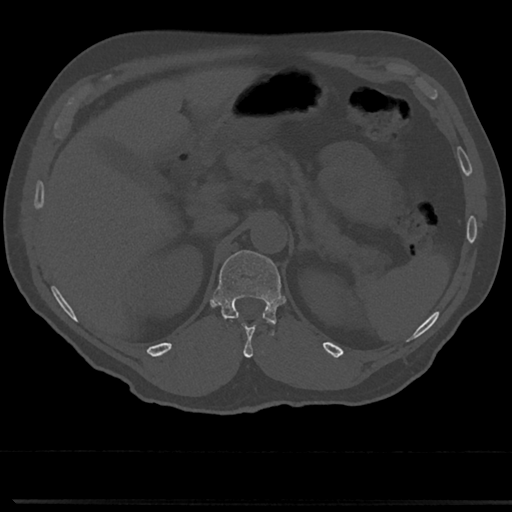
CT including the spine, one axial slice; slice 165 of 817 in the series (ordered by position); reconstruction kernel Br40s/3; bone window (W 1800 / L 400 HU); 512 × 512 image matrix, field of view 355 × 355 mm. Patient: male, 61 years. Case-level facts recorded for this patient, not image findings: primary cancer: prostate.
Structures marked on this image (semi-automatic segmentation, software-assisted and operator-edited):
- T11 vertebra: bounding box <231,324,276,357> (left, top, right, bottom; pixels)
- T12 vertebra: <214,249,285,337>